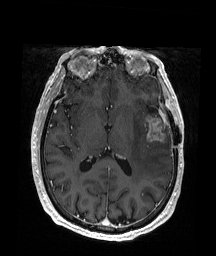
Brain MRI from a brain-tumour surgery series, one axial slice. Position 91 of 176 along the scan axis. T1-weighted post-contrast. 216 × 256 image matrix, field of view 219 × 260 mm. Case-level facts recorded for this patient, not image findings: histopathology: Glioblastoma; WHO grade: 4; IDH mutation: no.
Outlined on this slice (expert manual segmentation):
- tumour: bounding box (x1, y1, x2, y2) in pixels: (145, 115, 167, 144)